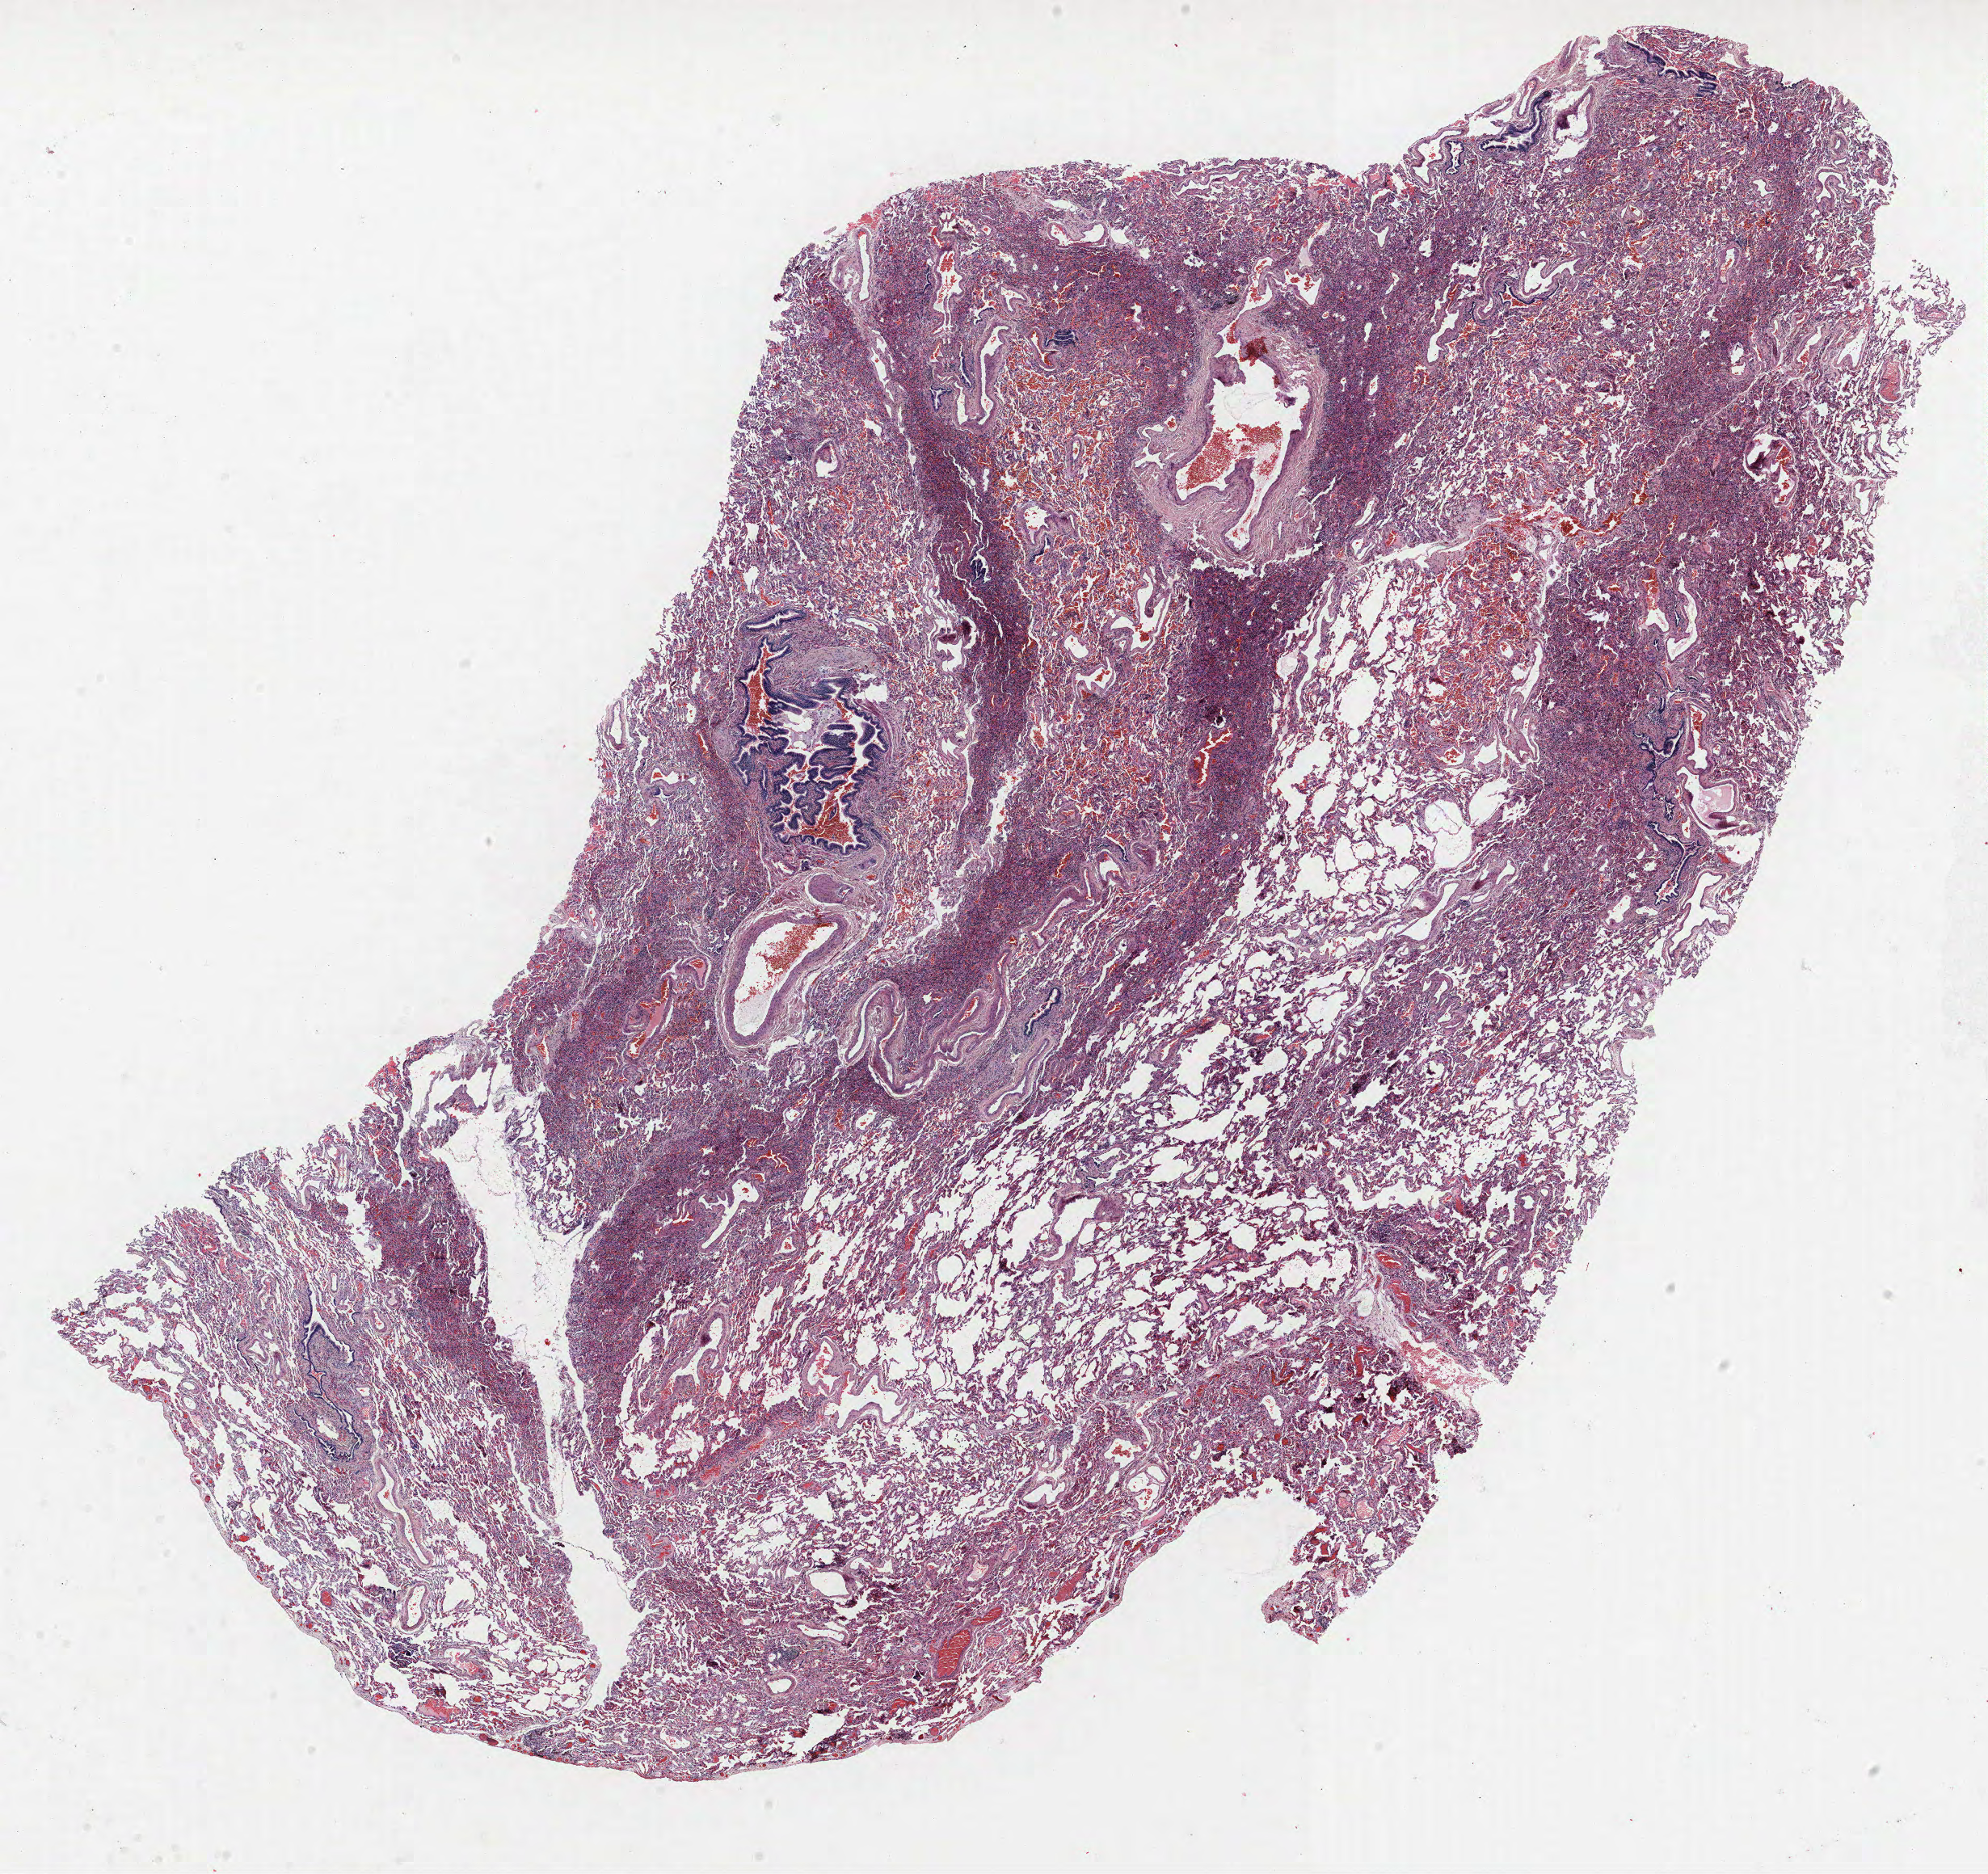
Whole-slide histology image, Hematoxylin and eosin (H&E) stained — shown as a low-resolution overview of the whole scanned area (about 19.7 x 18.6 mm, slide scanned at 40x), formalin-fixed paraffin-embedded (FFPE) section, lung tissue. Female patient, aged 59 at enrolment. Grade: well differentiated (G1).
Tumour size (pathology): 20 mm. Primary tumour location (clinical record): right middle lobe. Participant's lung-cancer diagnosis: Bronchiolo-alveolar carcinoma, non-mucinous (ICD-O-3 8252/3). Stage (AJCC 6th edition): IB.